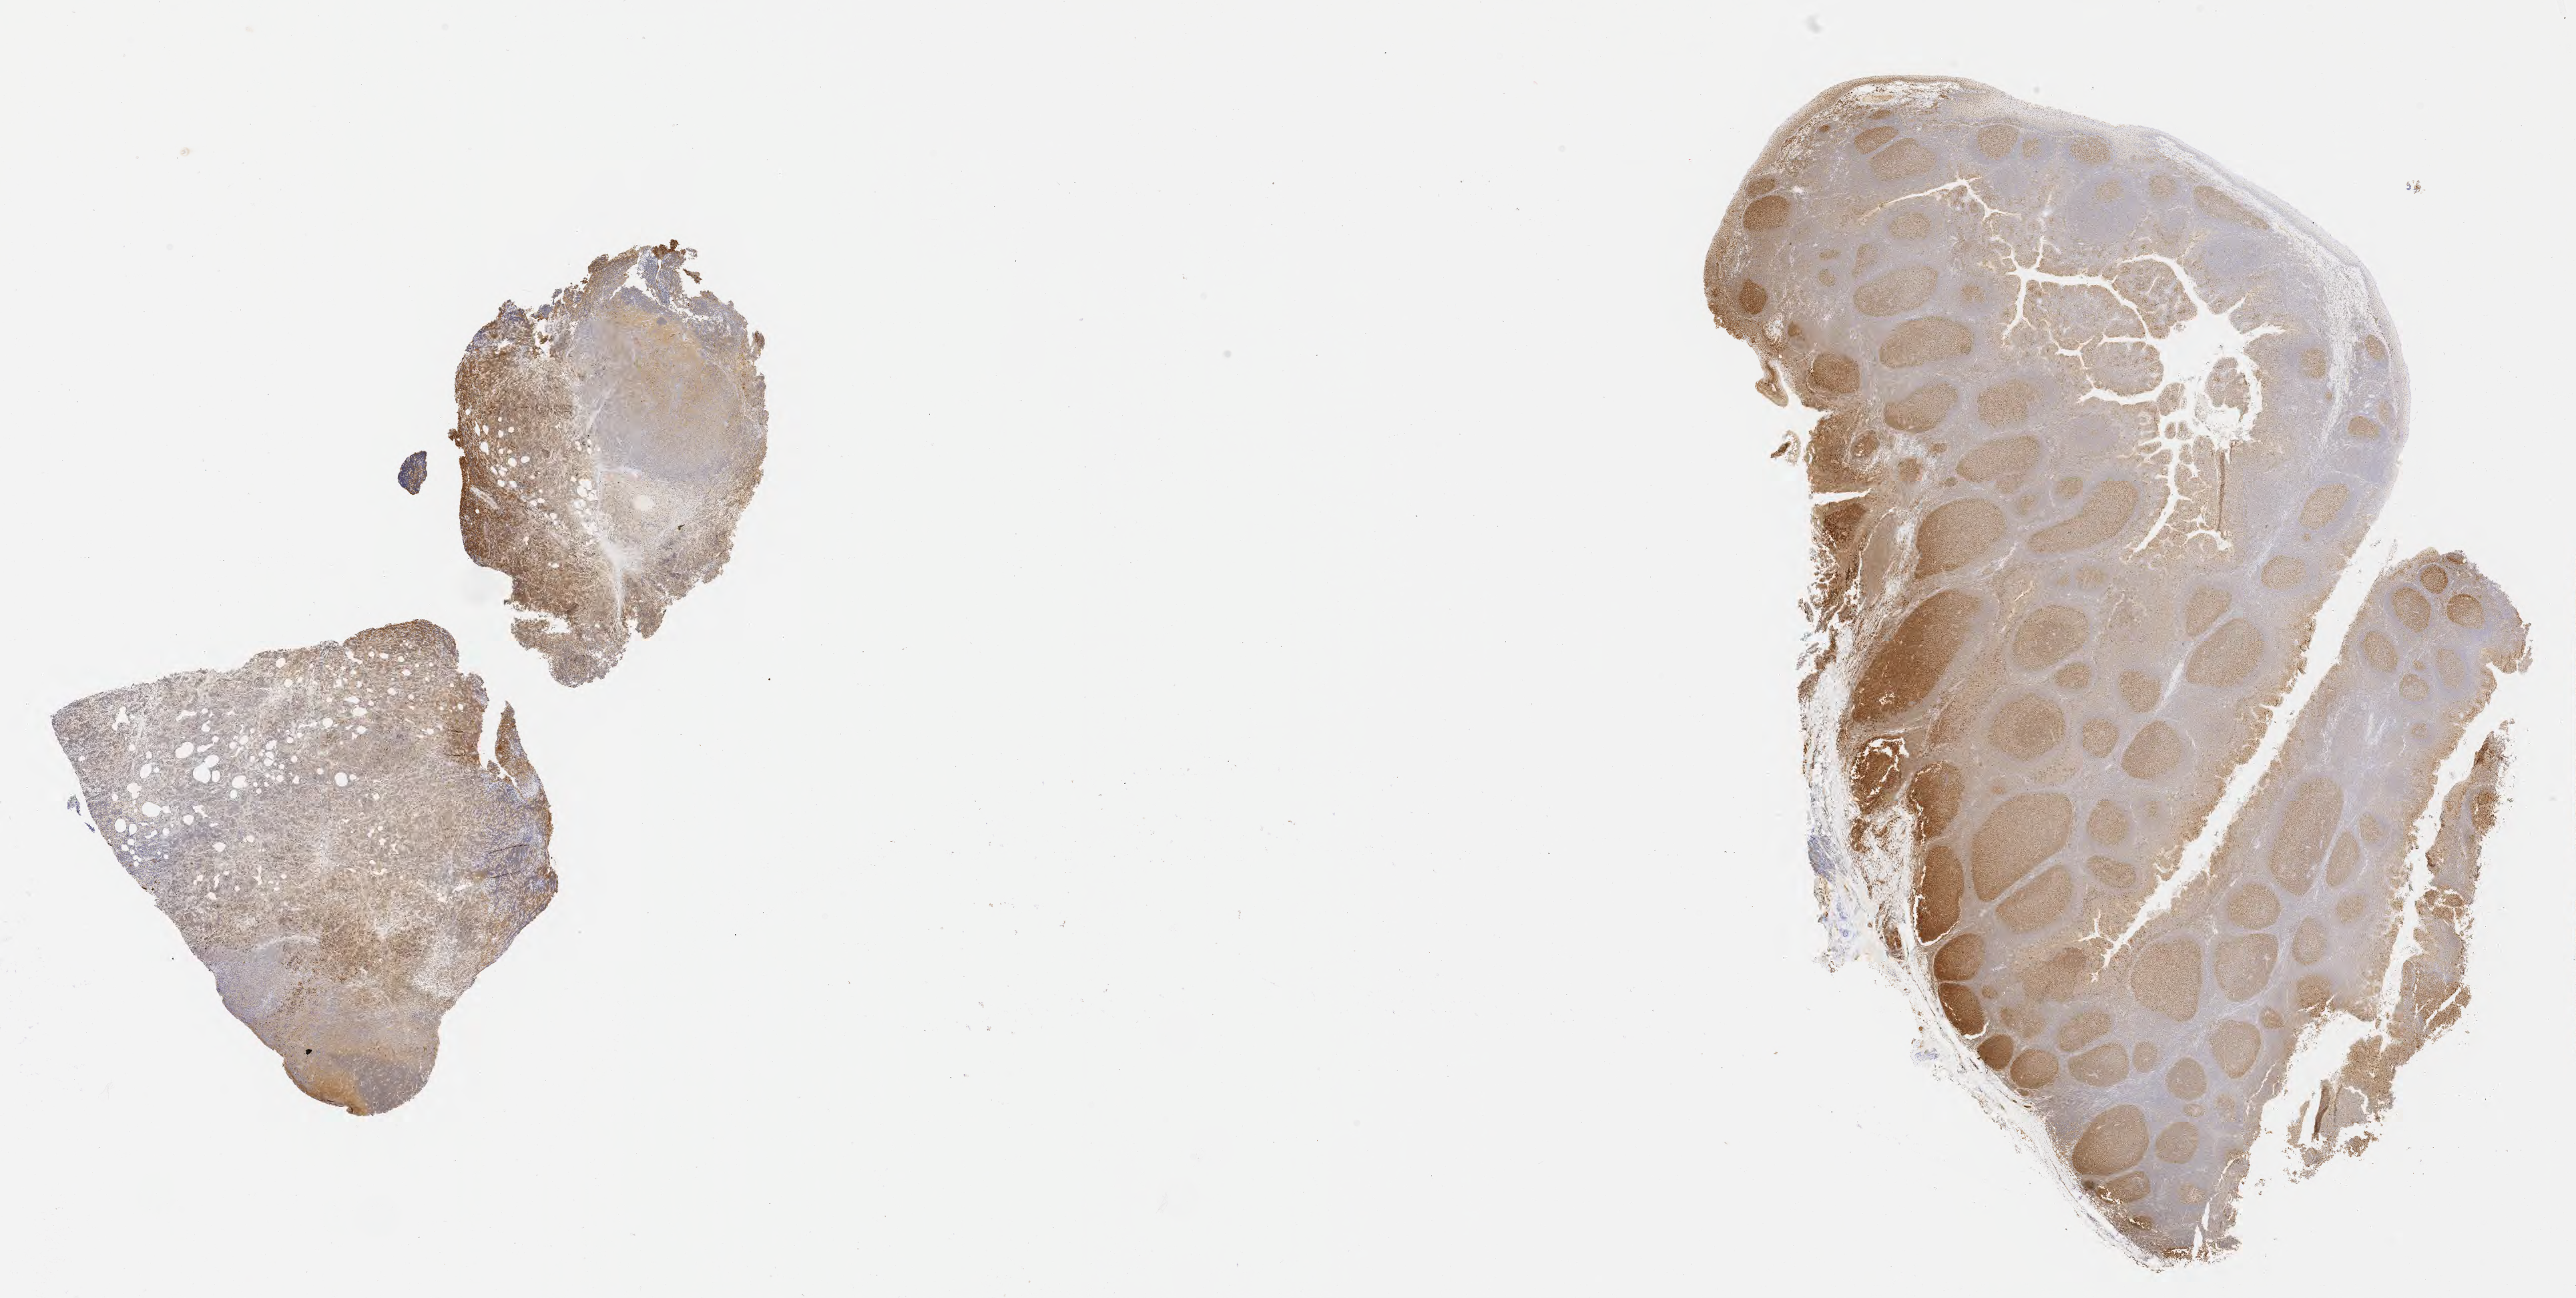
Whole-slide image, immunohistochemical stain for BCL6, low-resolution overview of the scanned area, about 31.2 x 15.7 mm; specimen: tumor tissue; anatomic site: mandible. Patient: male, age at initial diagnosis 7 years.
Histologic diagnosis: Burkitt lymphoma, NOS.